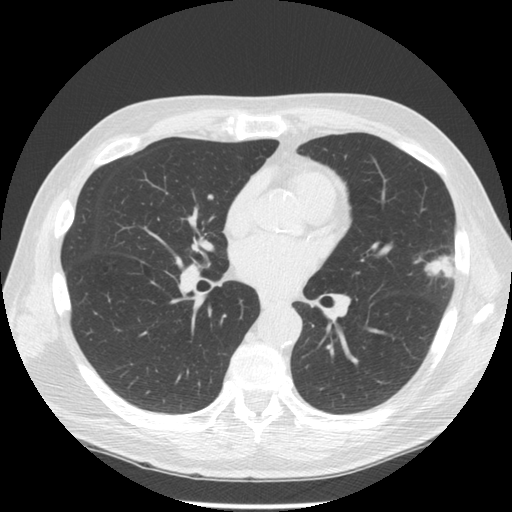
Low-dose screening chest CT, one axial slice; slice 71 of 134 in the series (ordered by position); reconstruction kernel STANDARD; lung window (W 1500 / L -600 HU); 2.5 mm slice thickness; 512 × 512 image matrix.
Outlined on this slice (manually delineated by an expert):
- lesion 1 (tumor, upper lobe of left lung): bounding box (x1, y1, x2, y2) in pixels: (425, 257, 455, 278)